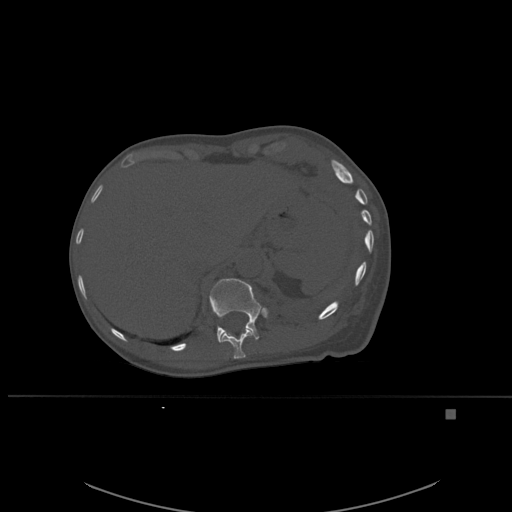
CT including the spine, one axial slice. Slice 289 of 537 in the series (ordered by position). Bone window (W 1800 / L 400 HU). 1.5 mm slice thickness. 512 × 512 image matrix, field of view 440 × 440 mm. Patient: female, 45 years. Case-level facts recorded for this patient, not image findings: primary cancer: lung.
Structures marked on this image (semi-automatically segmented with operator editing):
- T11 vertebra: box from (x=210, y=303) to (x=254, y=359) px
- T12 vertebra: (x=209, y=278)–(x=267, y=342)